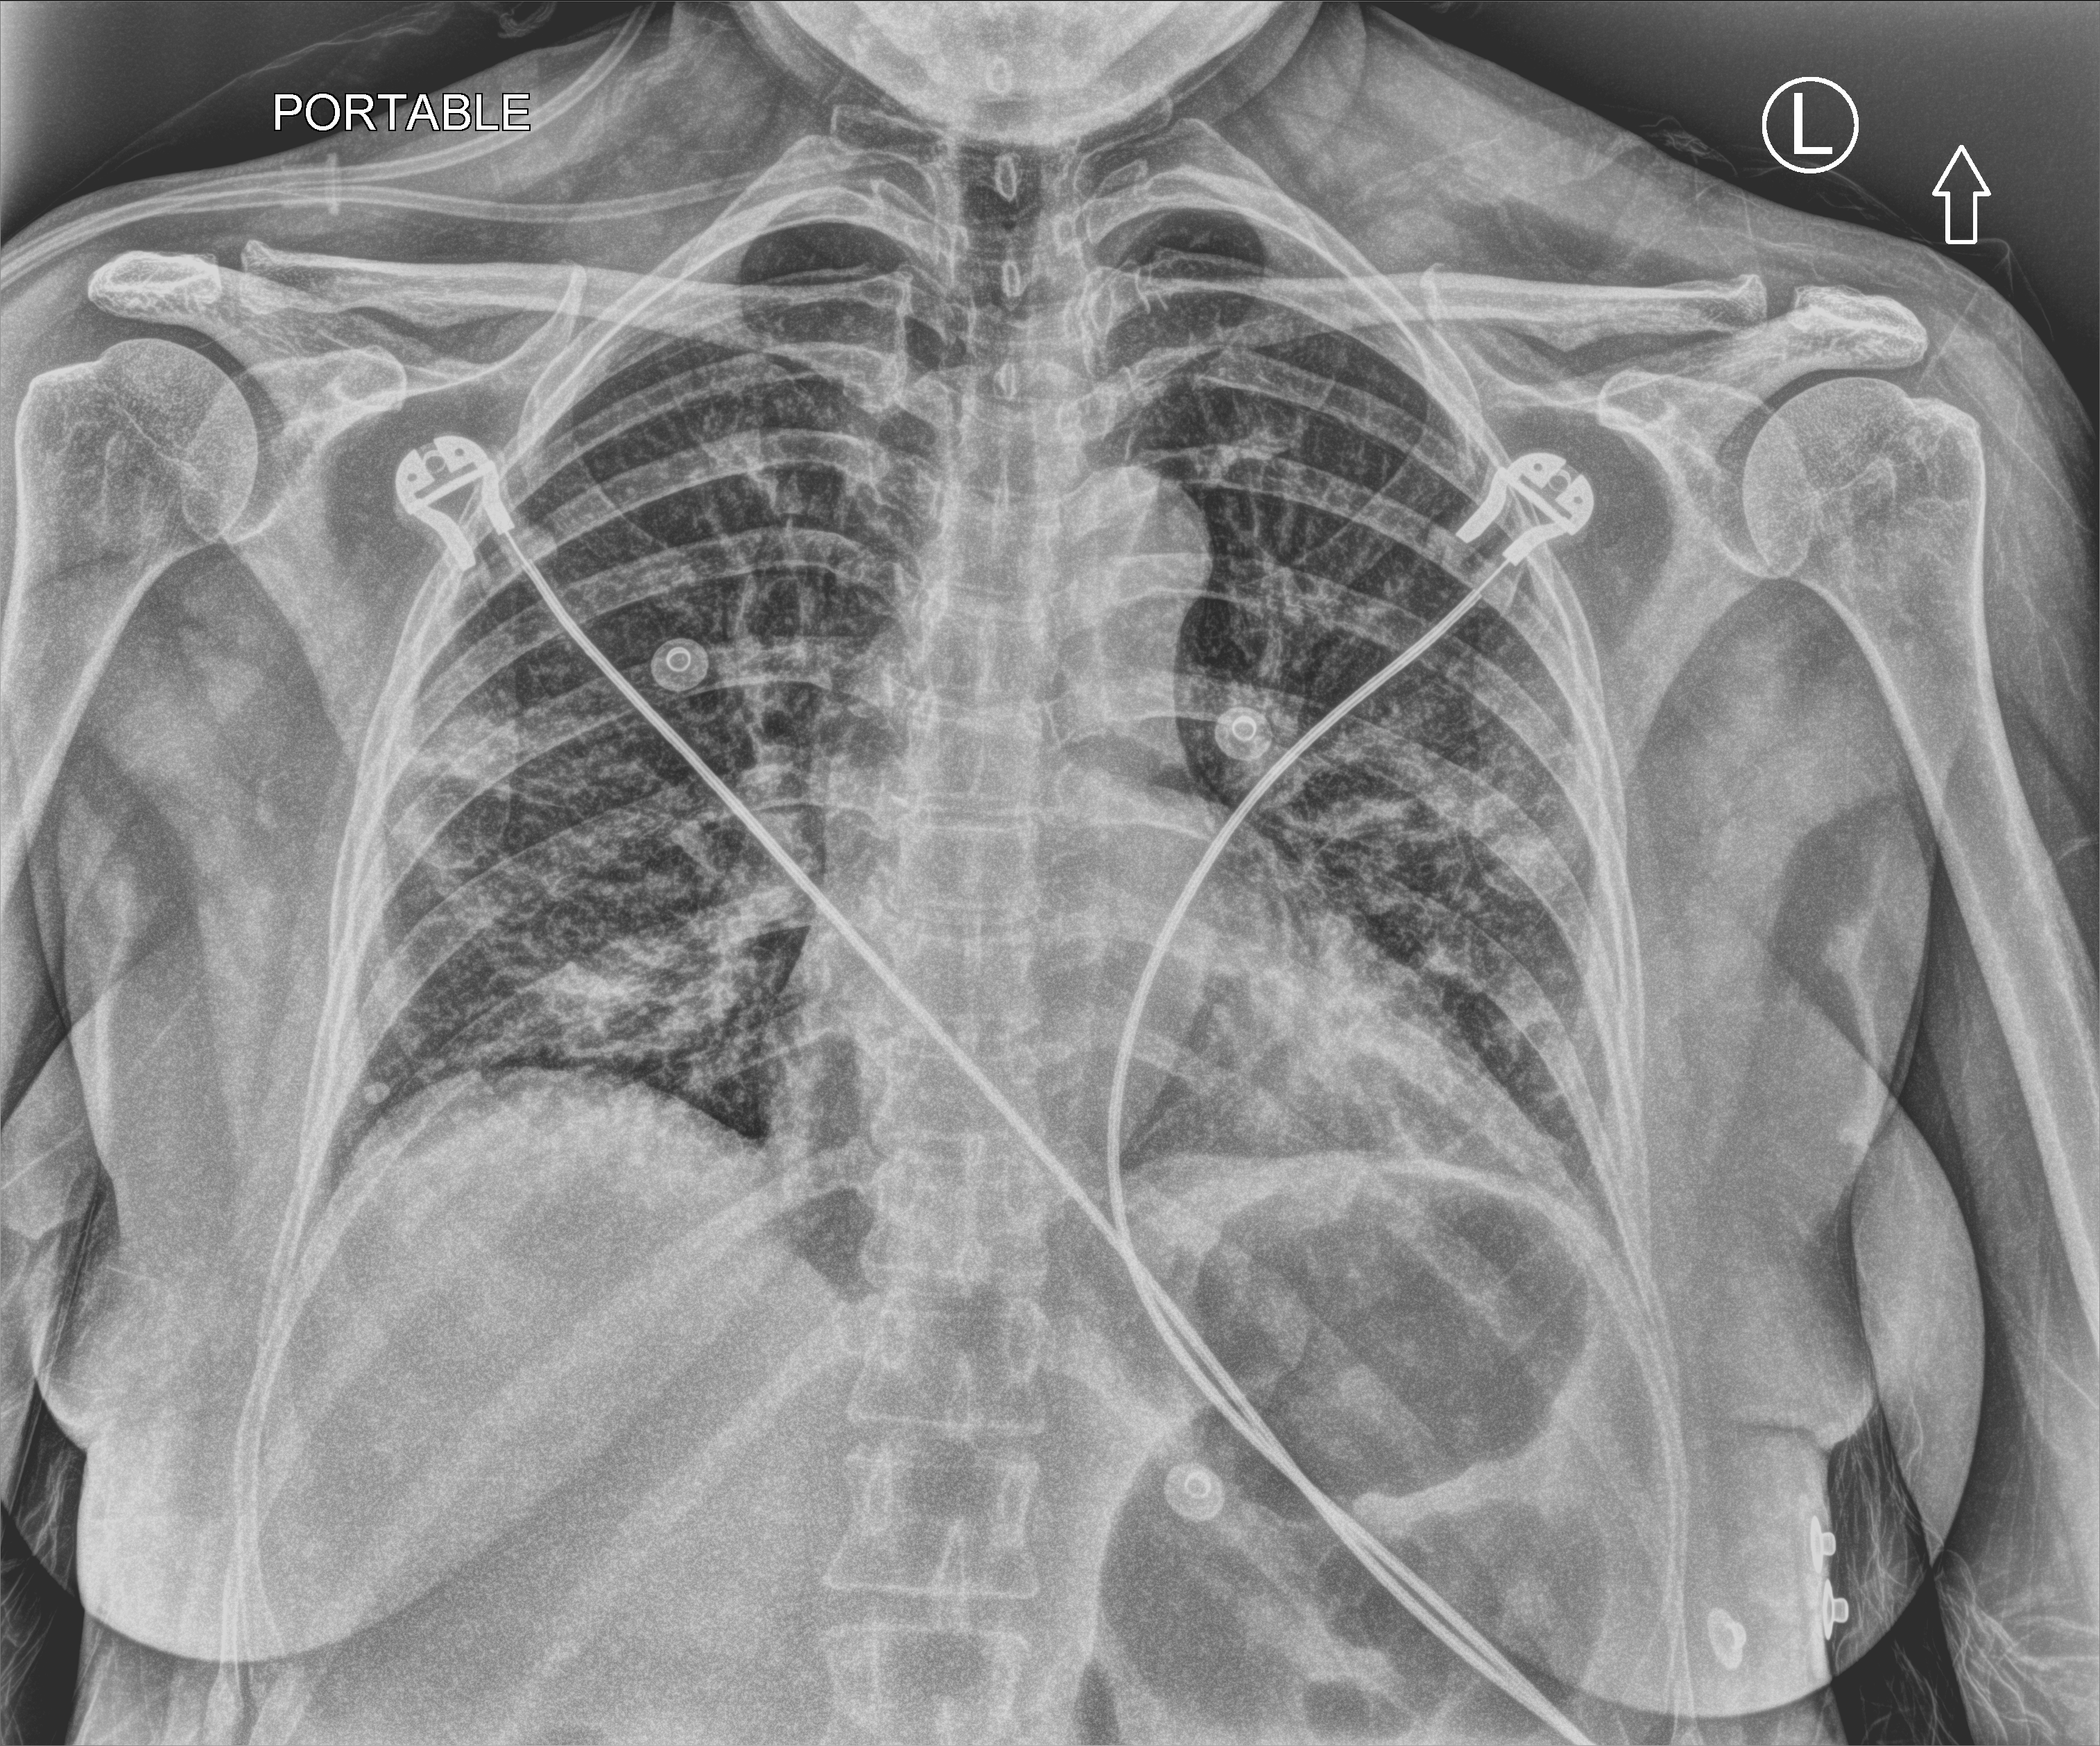
Bedside chest radiograph (computed radiography), anteroposterior (AP) projection. Patient hospitalised with COVID-19; female, aged 60–74 years.
Hospital-stay facts (about this admission, not read from this image; timing relative to this image not recorded): length of hospital stay: 1 day; mechanically ventilated during this hospital stay: no.